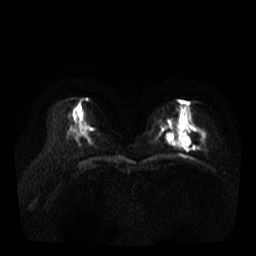
Breast MRI, one axial slice. Diffusion-weighted series; image 2 of 4 stored at this slice position (different b-values; order by instance number). 3 T. 5 mm slice thickness. 256 × 256 image matrix, field of view 320 × 320 mm. Female patient.
Annotated regions visible in this slice (outlined manually by an expert reader):
- tumour on diffusion-weighted imaging: box from (x=166, y=133) to (x=189, y=146) px